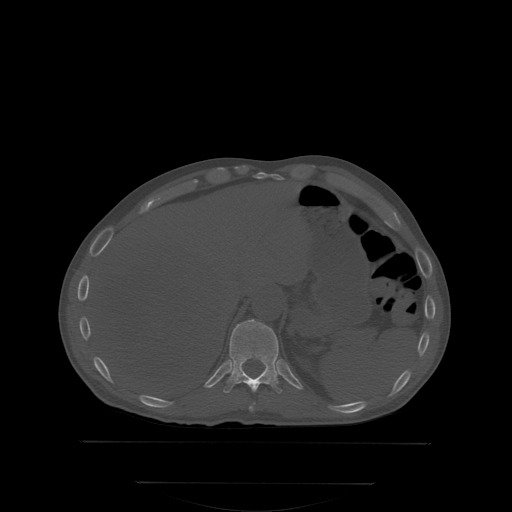
CT including the spine, one axial slice; position 181 of 350 along the scan axis; bone window (W 1800 / L 400 HU); 2.5 mm slice thickness; 512 × 512 image matrix. Patient: male, 58 years. From the clinical record (not read from this slice): primary cancer: prostate.
Structures marked on this image (semi-automatic segmentation, software-assisted and operator-edited):
- T10 vertebra: bounding box (x1, y1, x2, y2) in pixels: (251, 403, 255, 410)
- T11 vertebra: (219, 319, 288, 394)